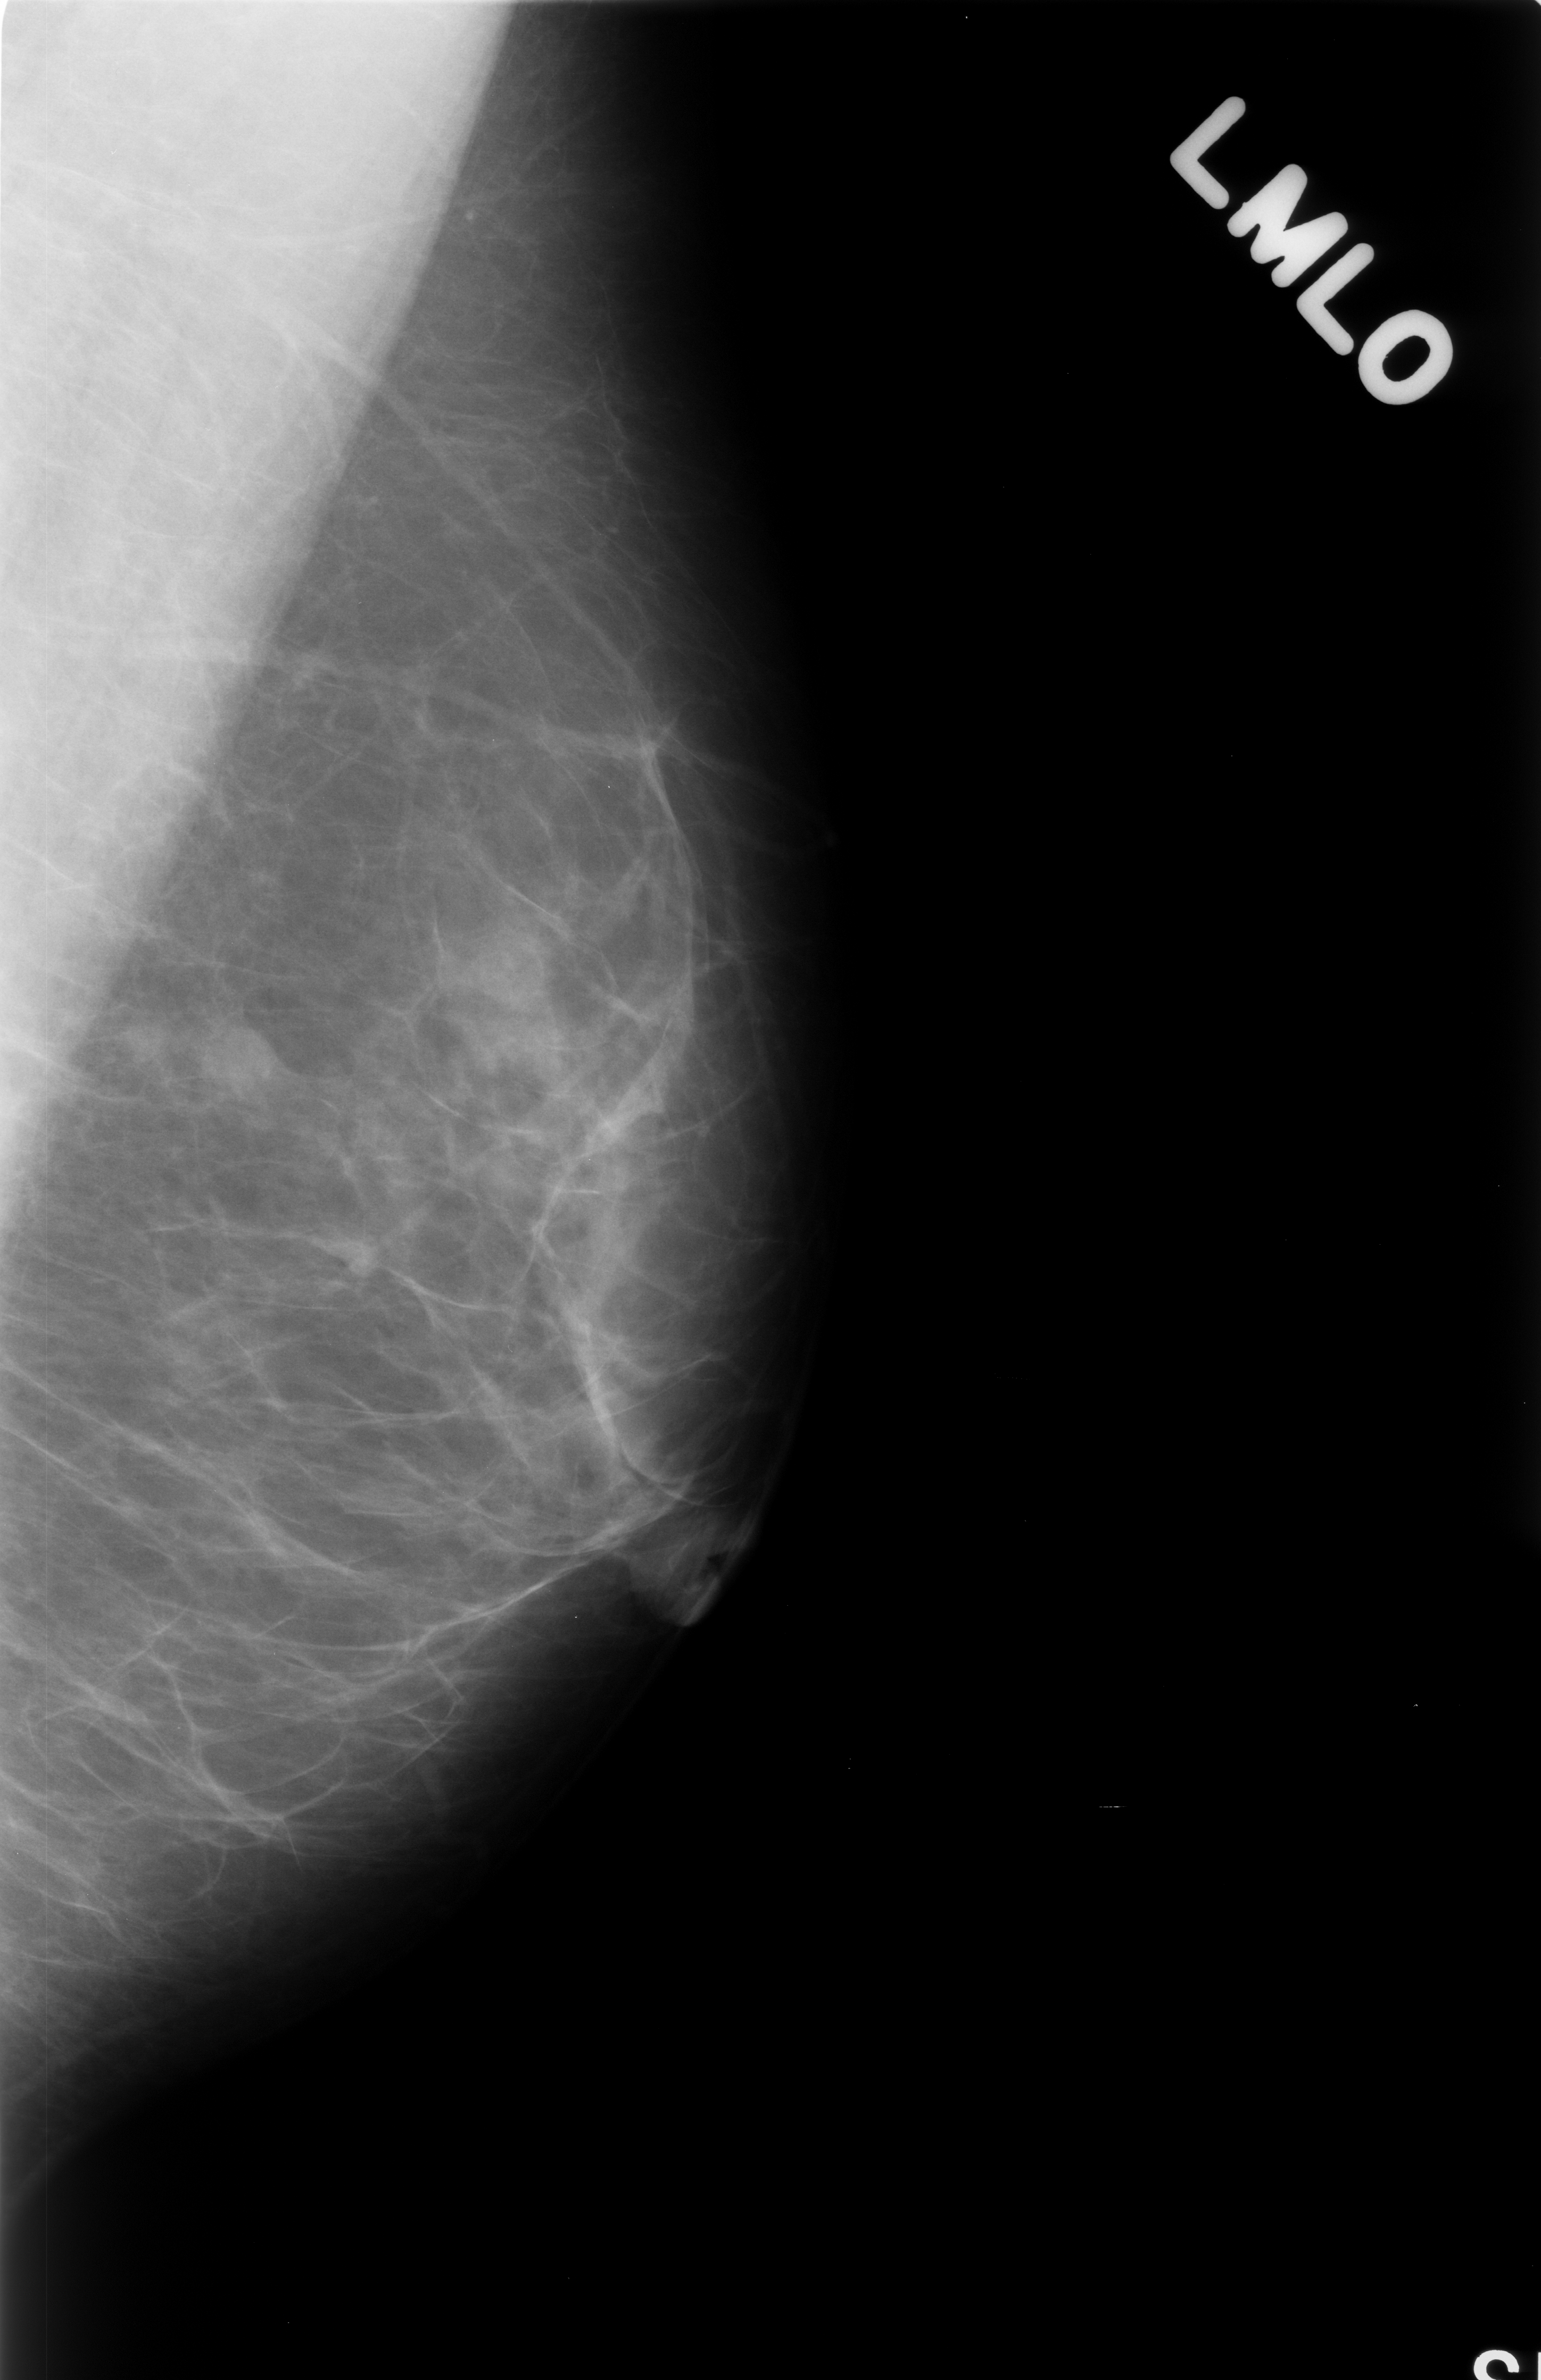
Digitized screen-film mammogram. Left breast. MLO view. 1541 × 2380 image matrix.
Expert-marked regions of interest on this film, with their recorded descriptors:
- mass, shape lobulated, margins circumscribed; BI-RADS assessment category 3; pathology (as recorded): benign: bounding box [x1, y1, x2, y2] px = [186, 997, 325, 1132]